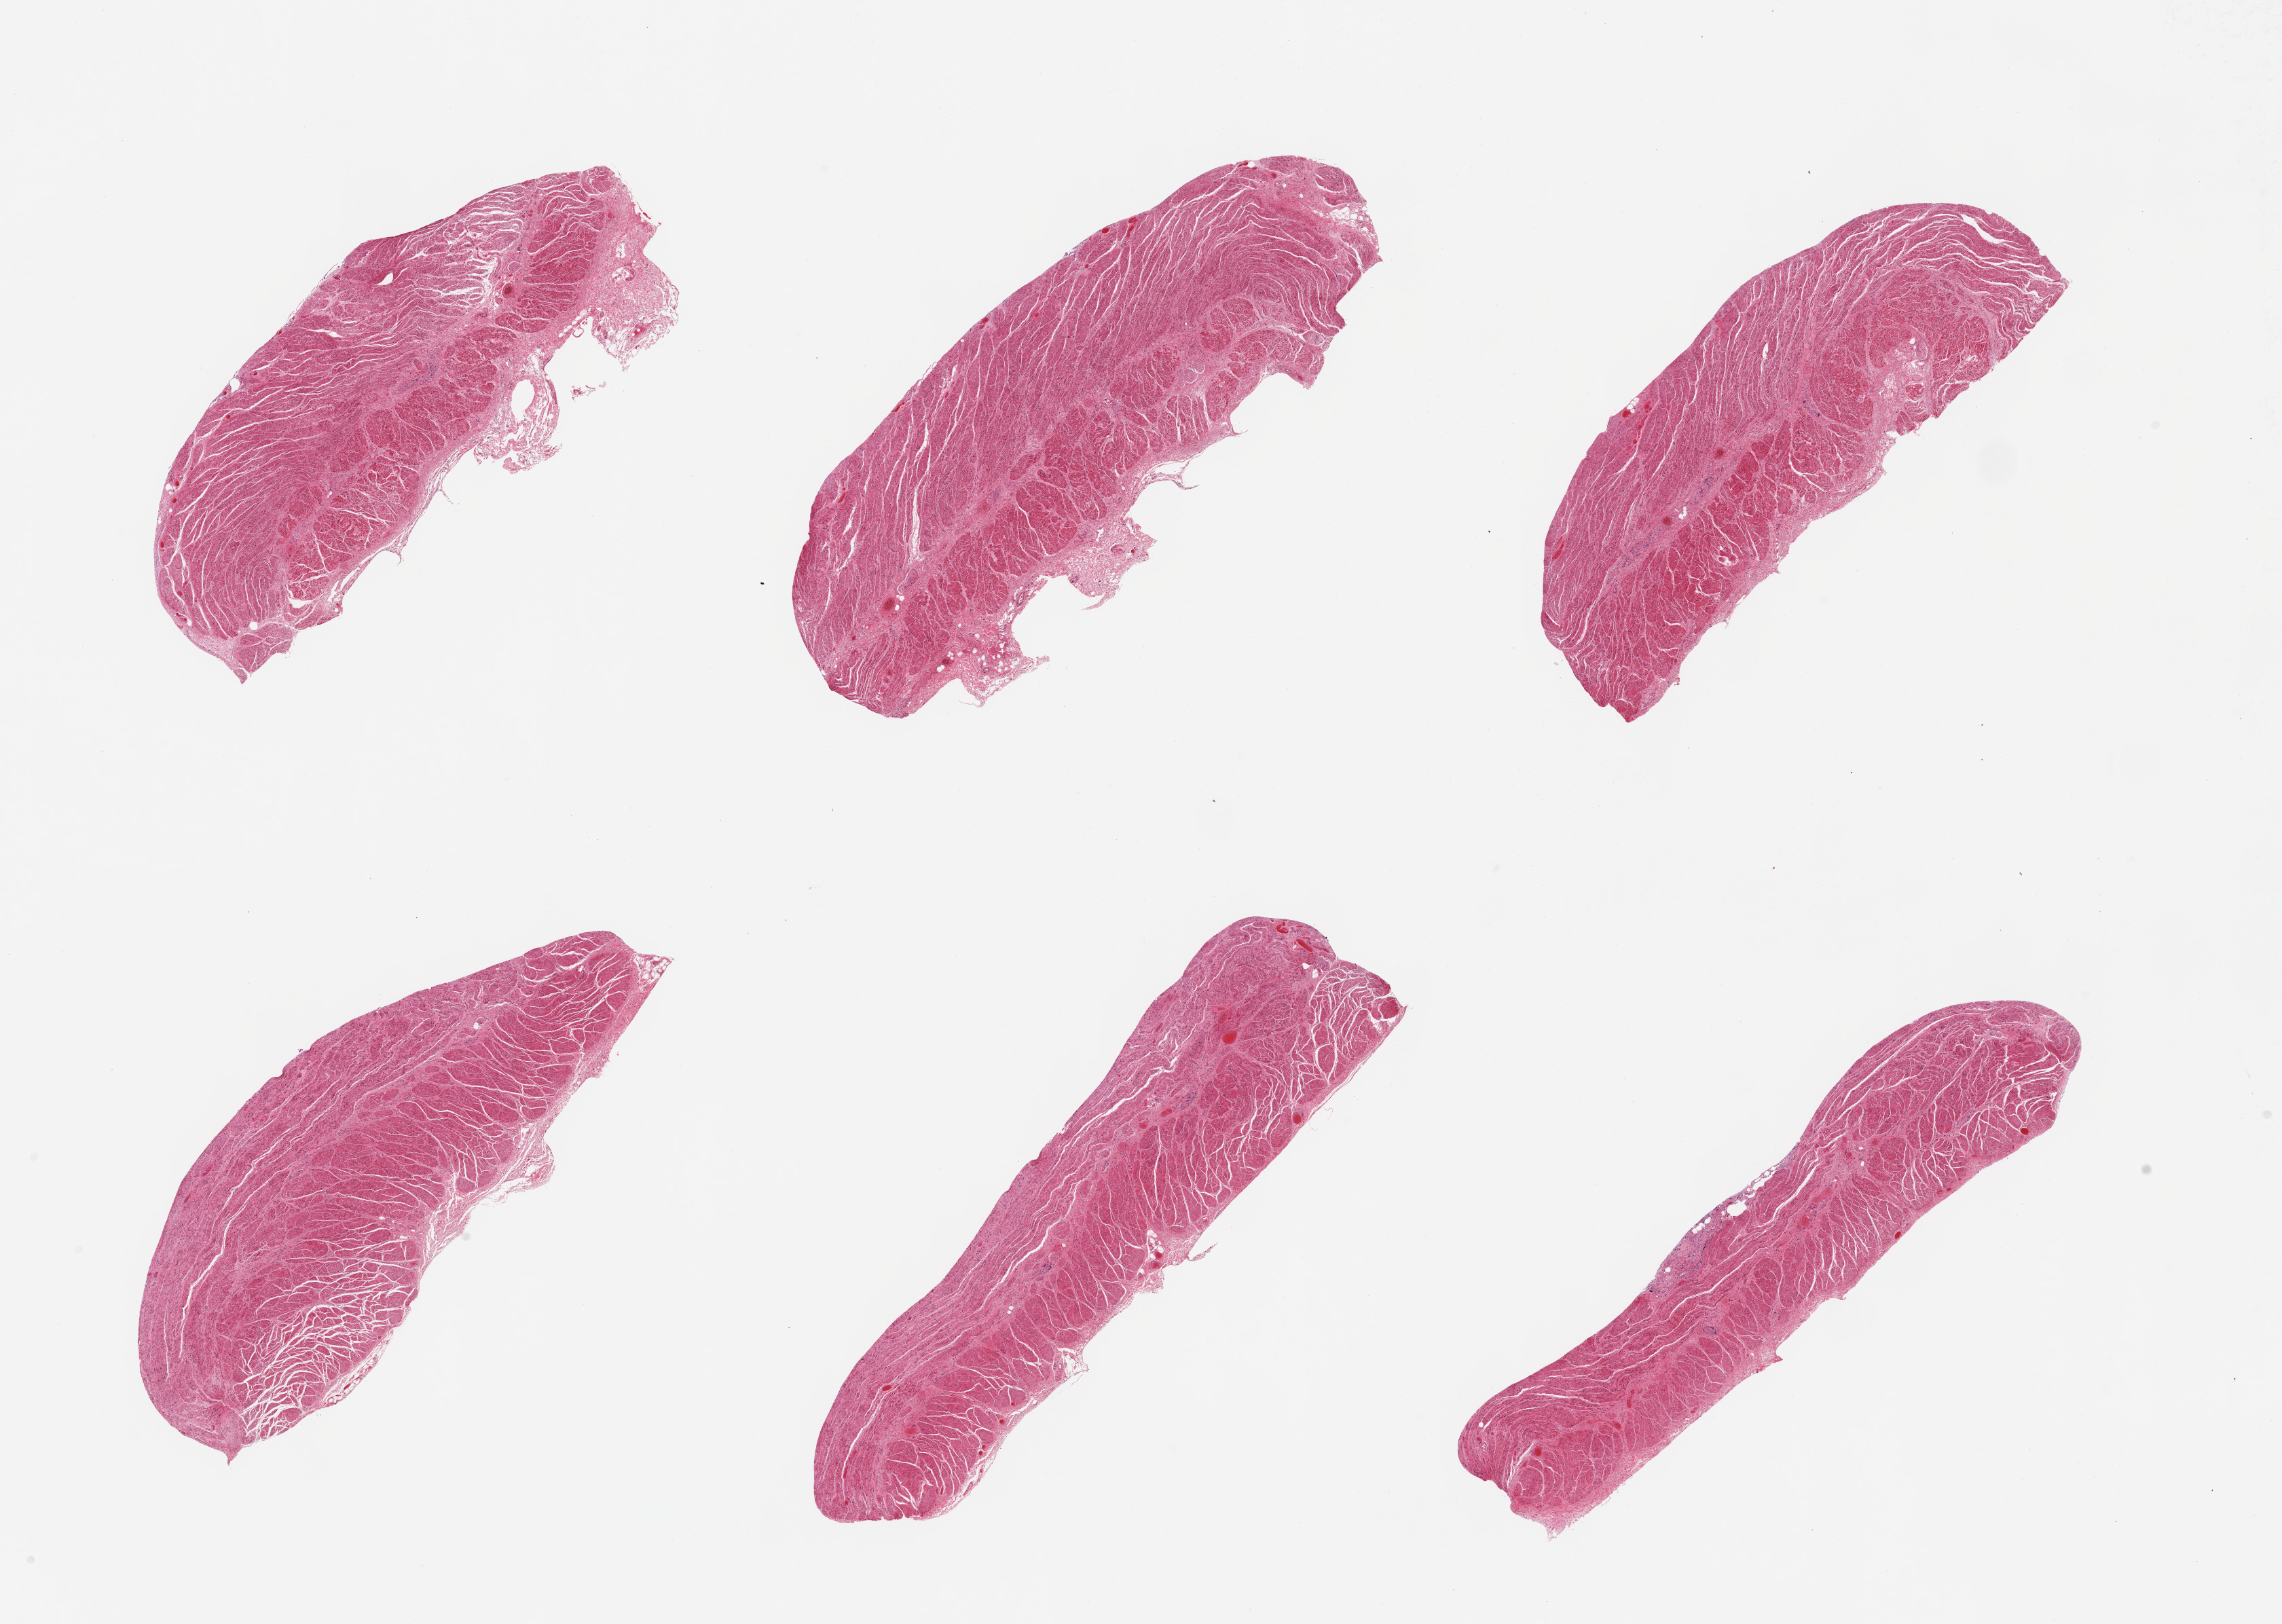
Whole-slide image, H&E stain, brightfield — shown as a low-resolution overview of the whole scanned area (about 26.6 x 18.9 mm). PAXgene-fixed paraffin-embedded (PFPE) section. Section of gastroesophageal junction (target tissue). Tissue donor sample. Donor sex: male.
Review note (as recorded): 6 pieces; well dissected.